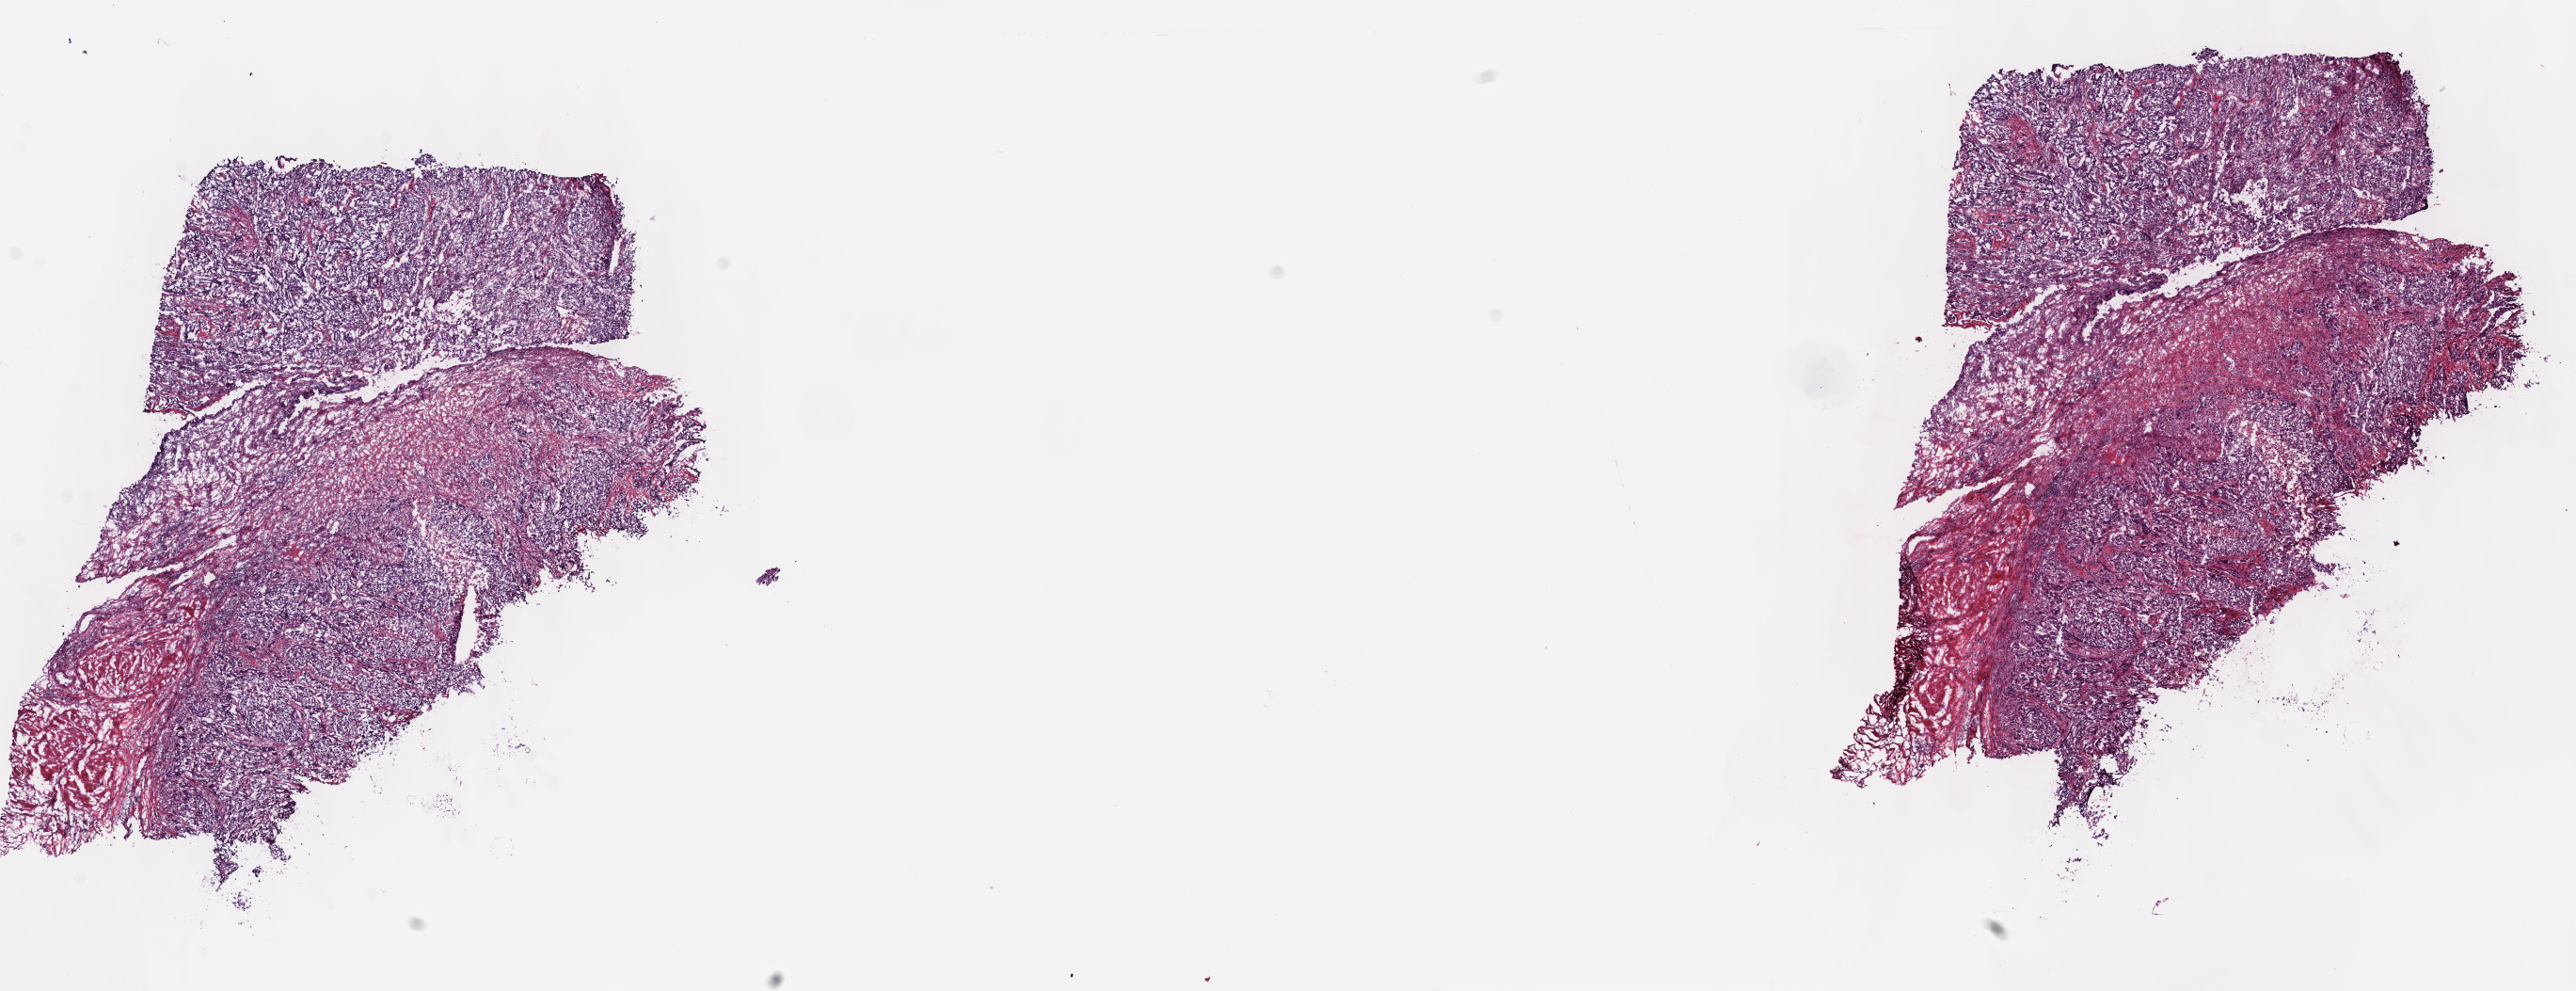
Whole-slide histology image, H&E, a low-resolution overview of the entire scanned area, about 22.1 x 8.5 mm (acquisition: 40x scan). Frozen section. Primary tumour sample from the bladder. Patient: male, age at initial diagnosis 62 years. Histologic grade: high grade. Composition of this section per pathologist review: tumour cells 70%, tumour nuclei 70%, normal cells 0%, stromal cells 30%, necrosis 0%. Infiltration values recorded for this section: lymphocyte infiltration 4%, monocyte infiltration 1%, neutrophil infiltration 5%.
Histologic diagnosis: Papillary transitional cell carcinoma. AJCC pathologic stage: IV (6th edition). Lymph nodes positive (case pathology): 1 of 23 examined.